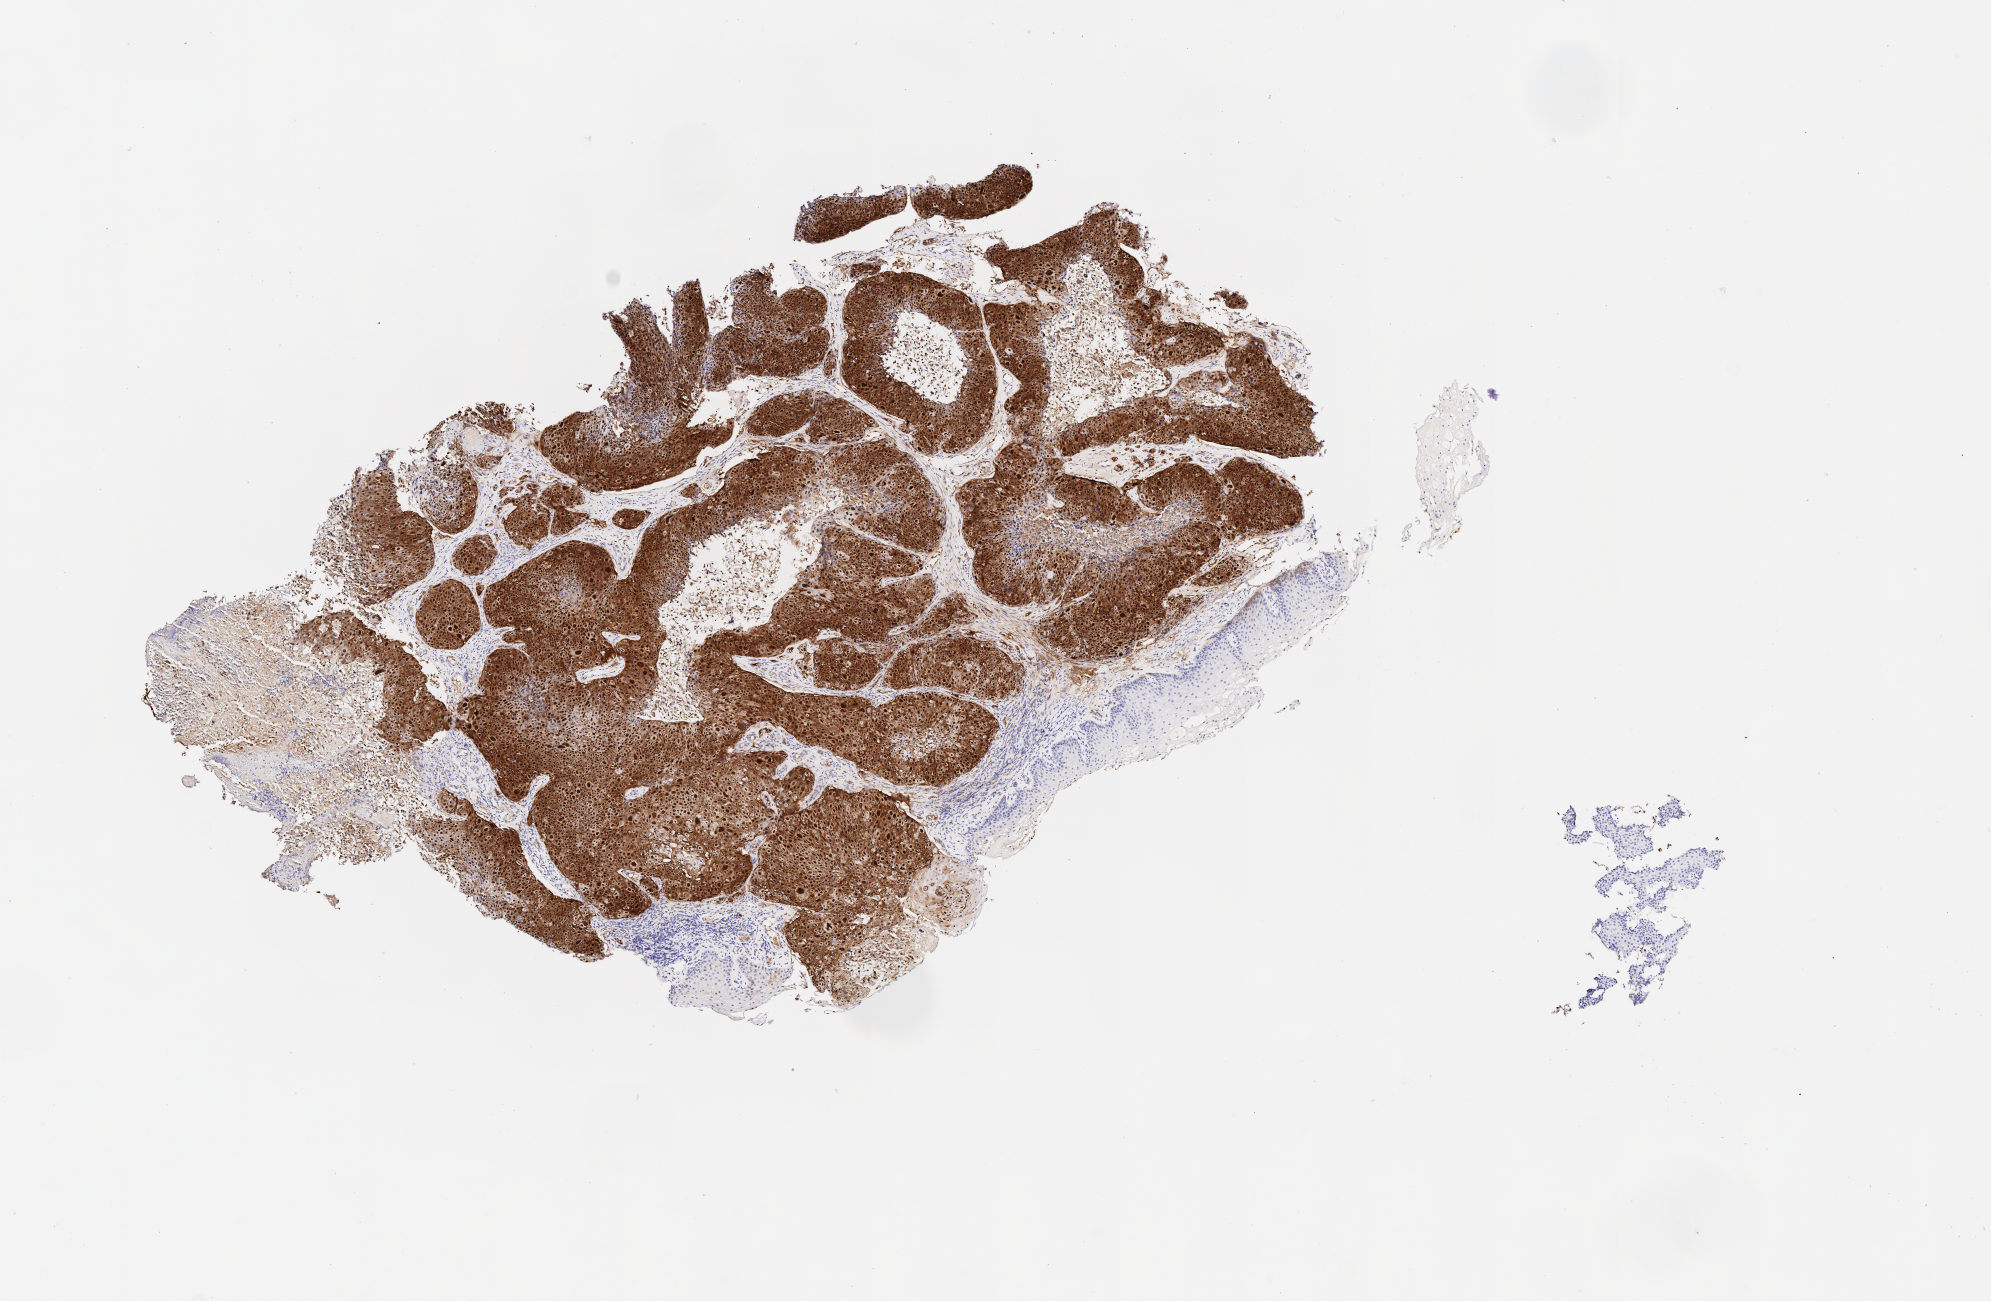
IHC for p16 (p16INK4a), whole-slide image — low-resolution overview of the scanned area, about 8.1 x 5.3 mm. Specimen: tumor tissue. Site: cervix. Patient female; age 32 years.
Histologic diagnosis: Squamous cell carcinoma, keratinizing, NOS.